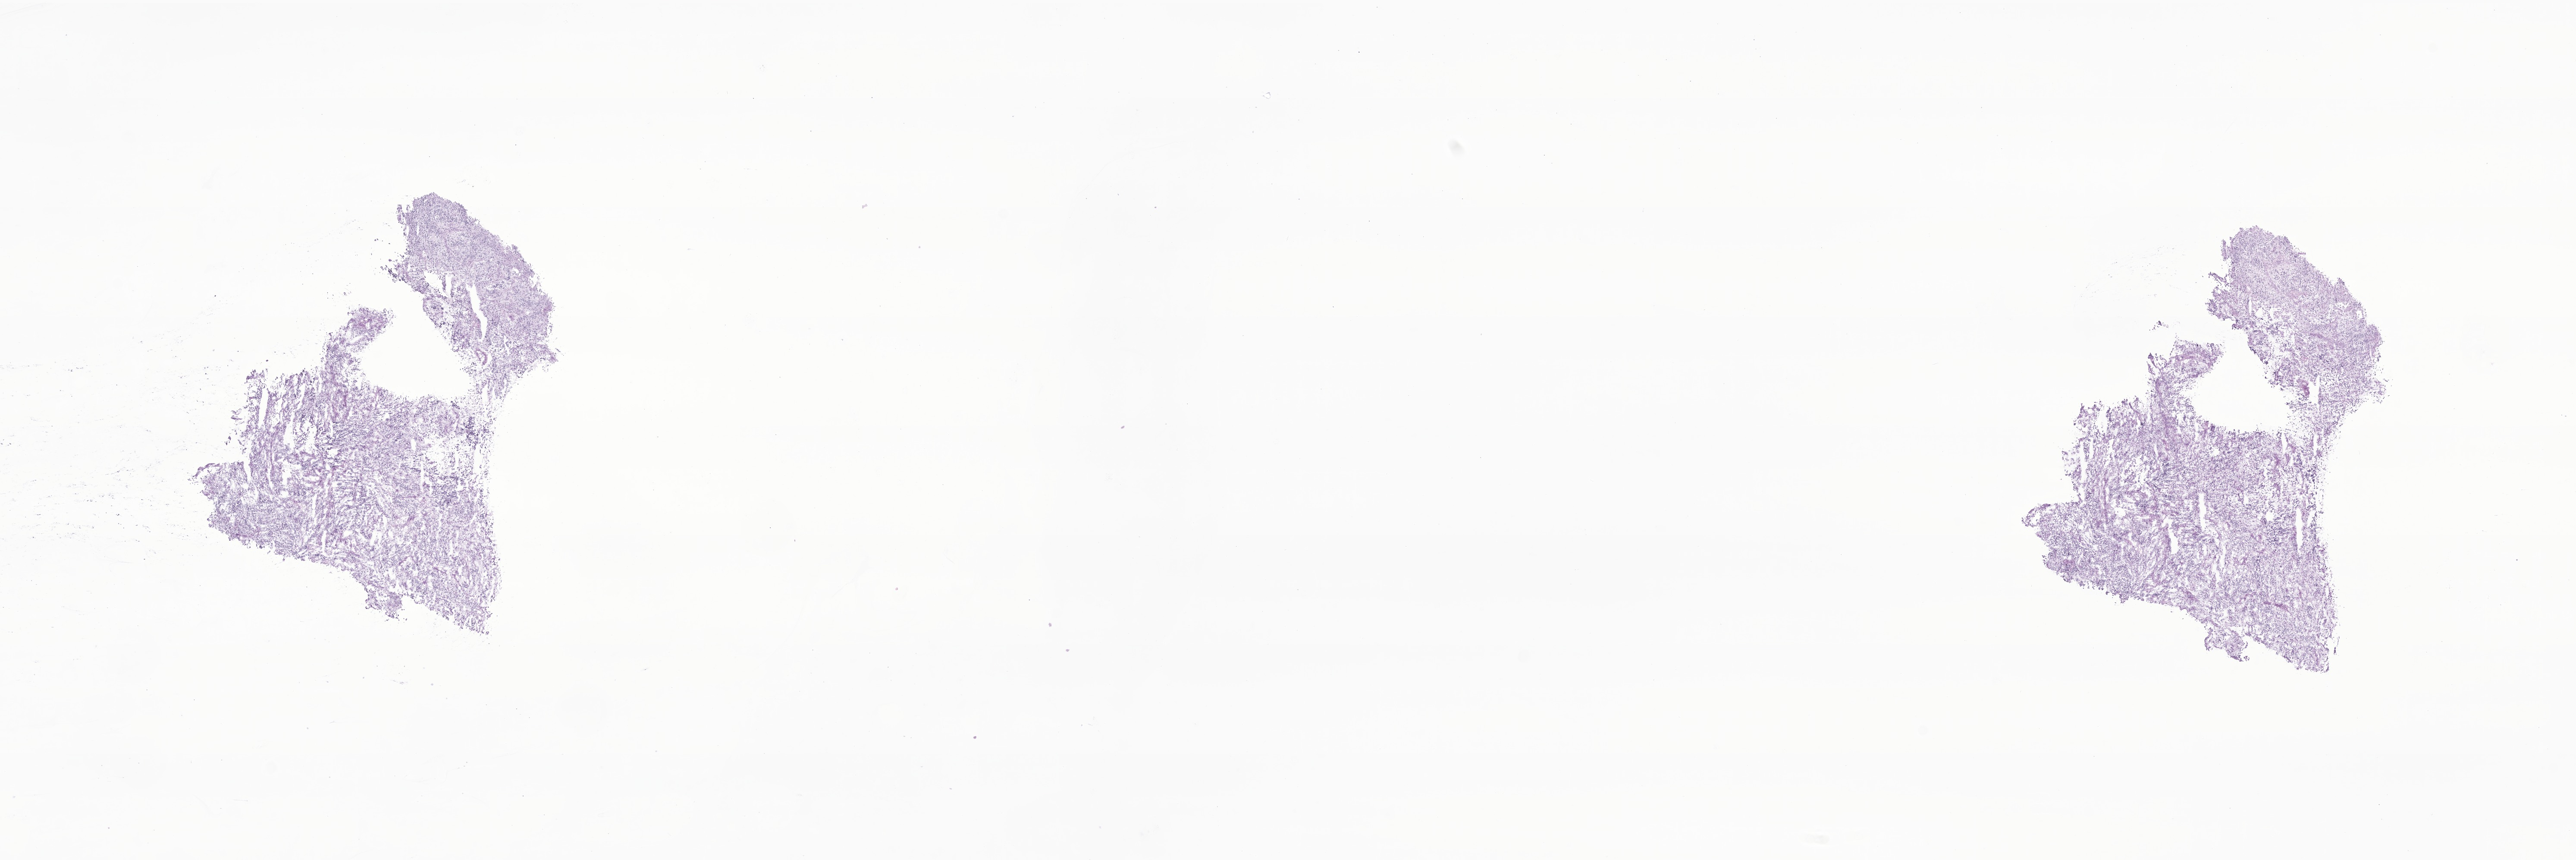
Digitized hematoxylin and eosin (H&E)-stained section of tumor tissue from the retroperitoneum — shown as a low-resolution overview of the whole scanned area (about 25.2 x 8.4 mm). Frozen section. Male patient, age 786 days.
• recorded diagnosis: Neuroblastoma, NOS